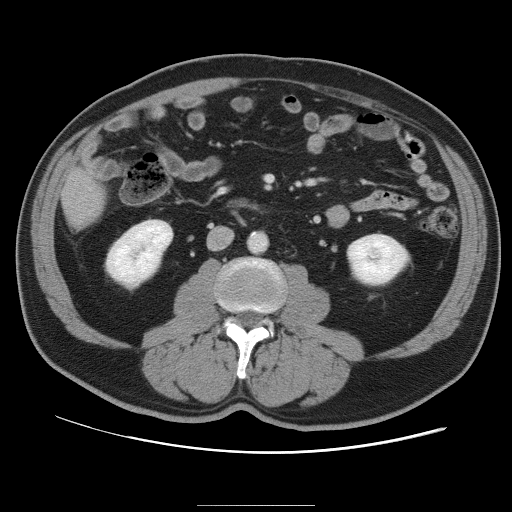
Contrast-enhanced abdominal CT, one axial slice. Position 23 of 105 along the scan axis. 120 kVp. Soft-tissue window (W 400 / L 40 HU). 512 × 512 image matrix. Male patient, age 64 years. From the clinical record (not read from this slice): diagnosis: colorectal cancer liver metastases, imaged before liver resection; multiple liver metastases: yes; largest metastasis: 3 cm; disease in both lobes: yes.
Annotated regions visible in this slice (outlined manually by an expert reader):
- liver: bounding box <64,169,105,224> (left, top, right, bottom; pixels)
- planned liver remnant (the part of the liver to remain after resection): <64,170,105,222>